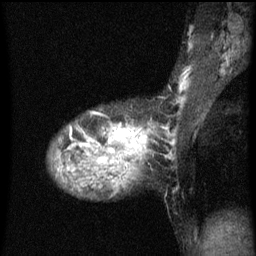
Breast MRI (dynamic contrast-enhanced), one sagittal slice; slice 38 of 60 in the series (ordered by position); dynamic contrast-enhanced series, image 2 of 3 at this slice position (ordered by acquisition); 1.5 T; TE 4.2 ms, TR 8 ms; 2 mm slice thickness; 256 × 256 image matrix, field of view 180 × 180 mm. Patient: female, 36 years.
Outlined on this slice (semi-automatic segmentation, software-assisted and operator-edited):
- analysis volume of interest (the breast-tissue region the enhancement analysis was run in; not a lesion): bounding box [x1, y1, x2, y2] px = [54, 126, 145, 161]
- tumour enhancement mask (voxels above the 70 % enhancement threshold inside the analysis volume of interest): [56, 126, 145, 161]